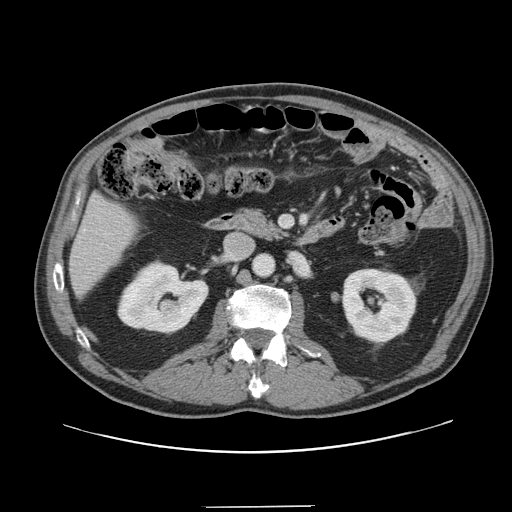
Contrast-enhanced abdominal CT, one axial slice. Position 59 of 139 along the scan axis. 120 kVp. Soft-tissue window (W 400 / L 40 HU). 2.5 mm slice thickness. 512 × 512 image matrix, field of view 397 × 397 mm. Male patient, age 64 years. From the clinical record (not read from this slice): diagnosis: colorectal cancer liver metastases, imaged before liver resection; multiple liver metastases: yes; largest metastasis: 3.5 cm; chemotherapy before resection: yes.
Outlined on this slice (expert manual segmentation):
- liver: bounding box [x1, y1, x2, y2] px = [70, 197, 138, 294]
- planned liver remnant (the part of the liver to remain after resection): [70, 197, 139, 293]